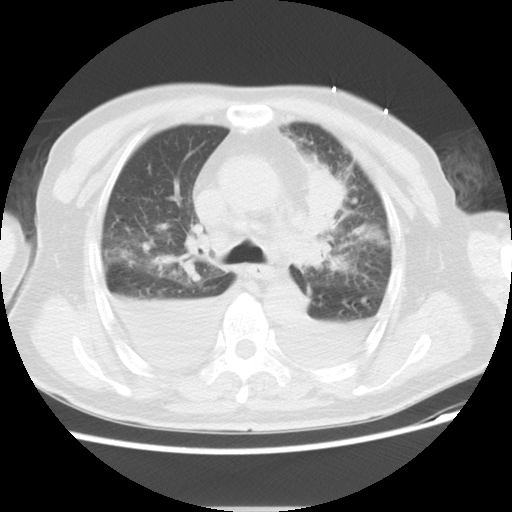
Chest CT, one axial slice. Slice 16 of 21 in the series (ordered by position). Reconstruction kernel STANDARD. 120 kVp. Lung window (W 1500 / L -600 HU). 5 mm slice thickness. 512 × 512 image matrix, field of view 350 × 350 mm. Patient: male, 66 years. Case-level facts recorded for this patient, not image findings: clinical TNM (as recorded): T1c N0 M0.
Structures marked on this image (bounding box drawn by a radiologist):
- lung tumour (recorded histology: adenocarcinoma): bounding box (x1, y1, x2, y2) in pixels: (304, 159, 344, 248)